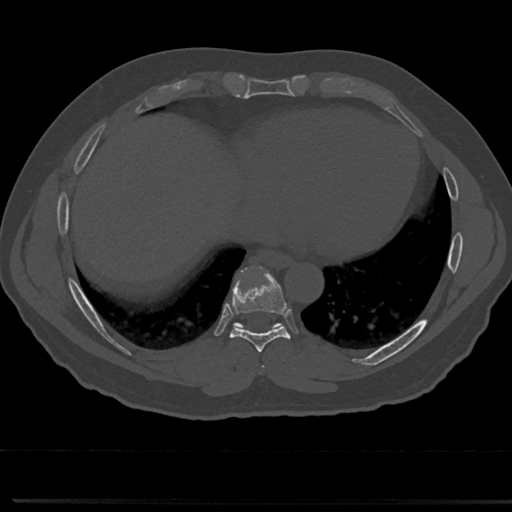
CT including the spine, one axial slice. Reconstruction kernel Br40s/3. 120 kVp. Bone window (W 1800 / L 400 HU). 0.5 mm slice thickness. 512 × 512 image matrix, field of view 355 × 355 mm. Male patient, age 61 years. From the clinical record (not read from this slice): primary cancer: prostate.
Structures marked on this image (semi-automatically segmented with operator editing):
- T7 vertebra: box from (x=255, y=341) to (x=269, y=377) px
- T8 vertebra: (x=215, y=271)–(x=305, y=354)